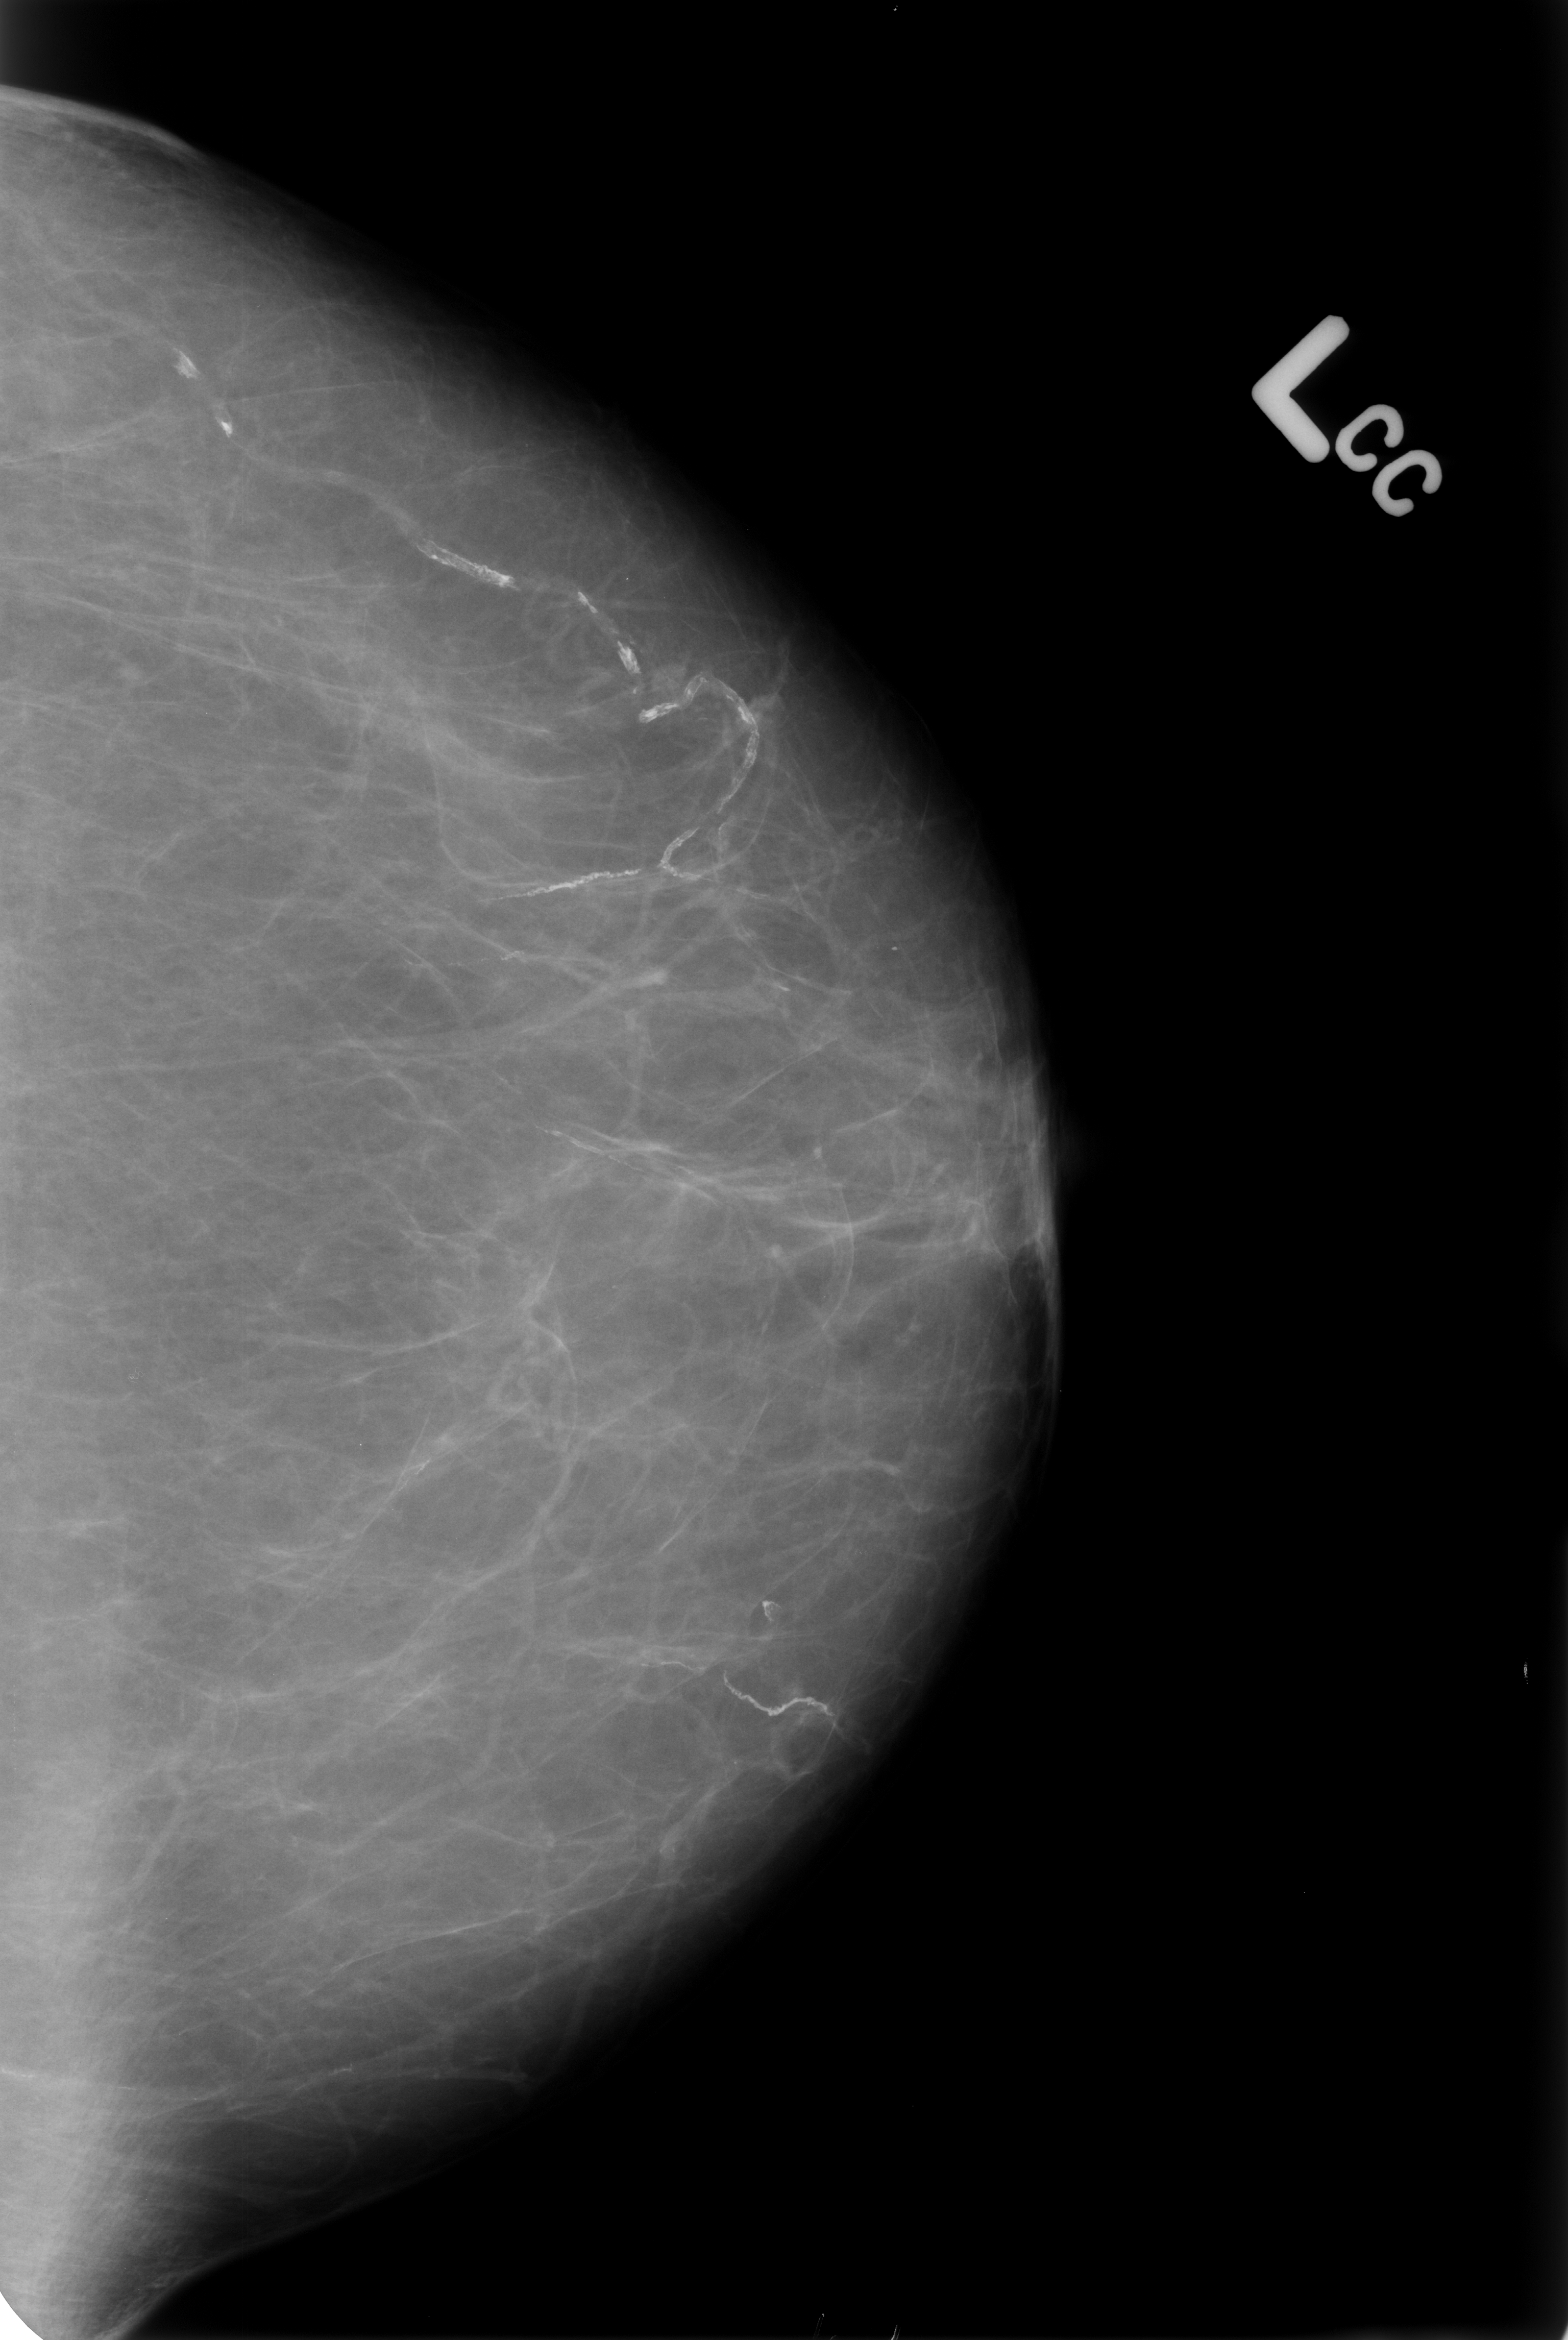
Scanned film-screen mammogram; left breast; craniocaudal (CC) view; breast composition: almost entirely fatty (BI-RADS density category 1 of 4); 1568 × 2340 image matrix.
Expert-marked regions of interest on this film, with their recorded descriptors:
- Finding 1 of 2: calcifications, morphology vascular; BI-RADS assessment category 2; subtlety rating 5 on a 1 (subtle) to 5 (obvious) scale; outcome (as recorded, no biopsy): benign without callback (not worked up further): bounding box [x1, y1, x2, y2] px = [73, 277, 801, 920]
- Finding 2 of 2: calcifications, morphology vascular; BI-RADS assessment category 2; subtlety rating 5 on a 1 (subtle) to 5 (obvious) scale; benign; no additional work-up was recommended (outcome (as recorded, no biopsy): benign without callback): [665, 1633, 891, 1757]